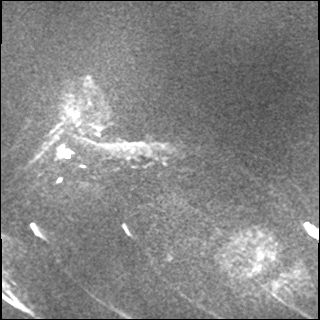
Breast MRI, one axial slice; diffusion-weighted series; image 2 of 4 stored at this slice position (different b-values; order by instance number); 1.5 T; 4 mm slice thickness; 320 × 320 image matrix, field of view 320 × 320 mm. Female patient.
Annotated regions visible in this slice (manually delineated by an expert):
- tumour on diffusion-weighted imaging: box from (x=61, y=149) to (x=71, y=159) px